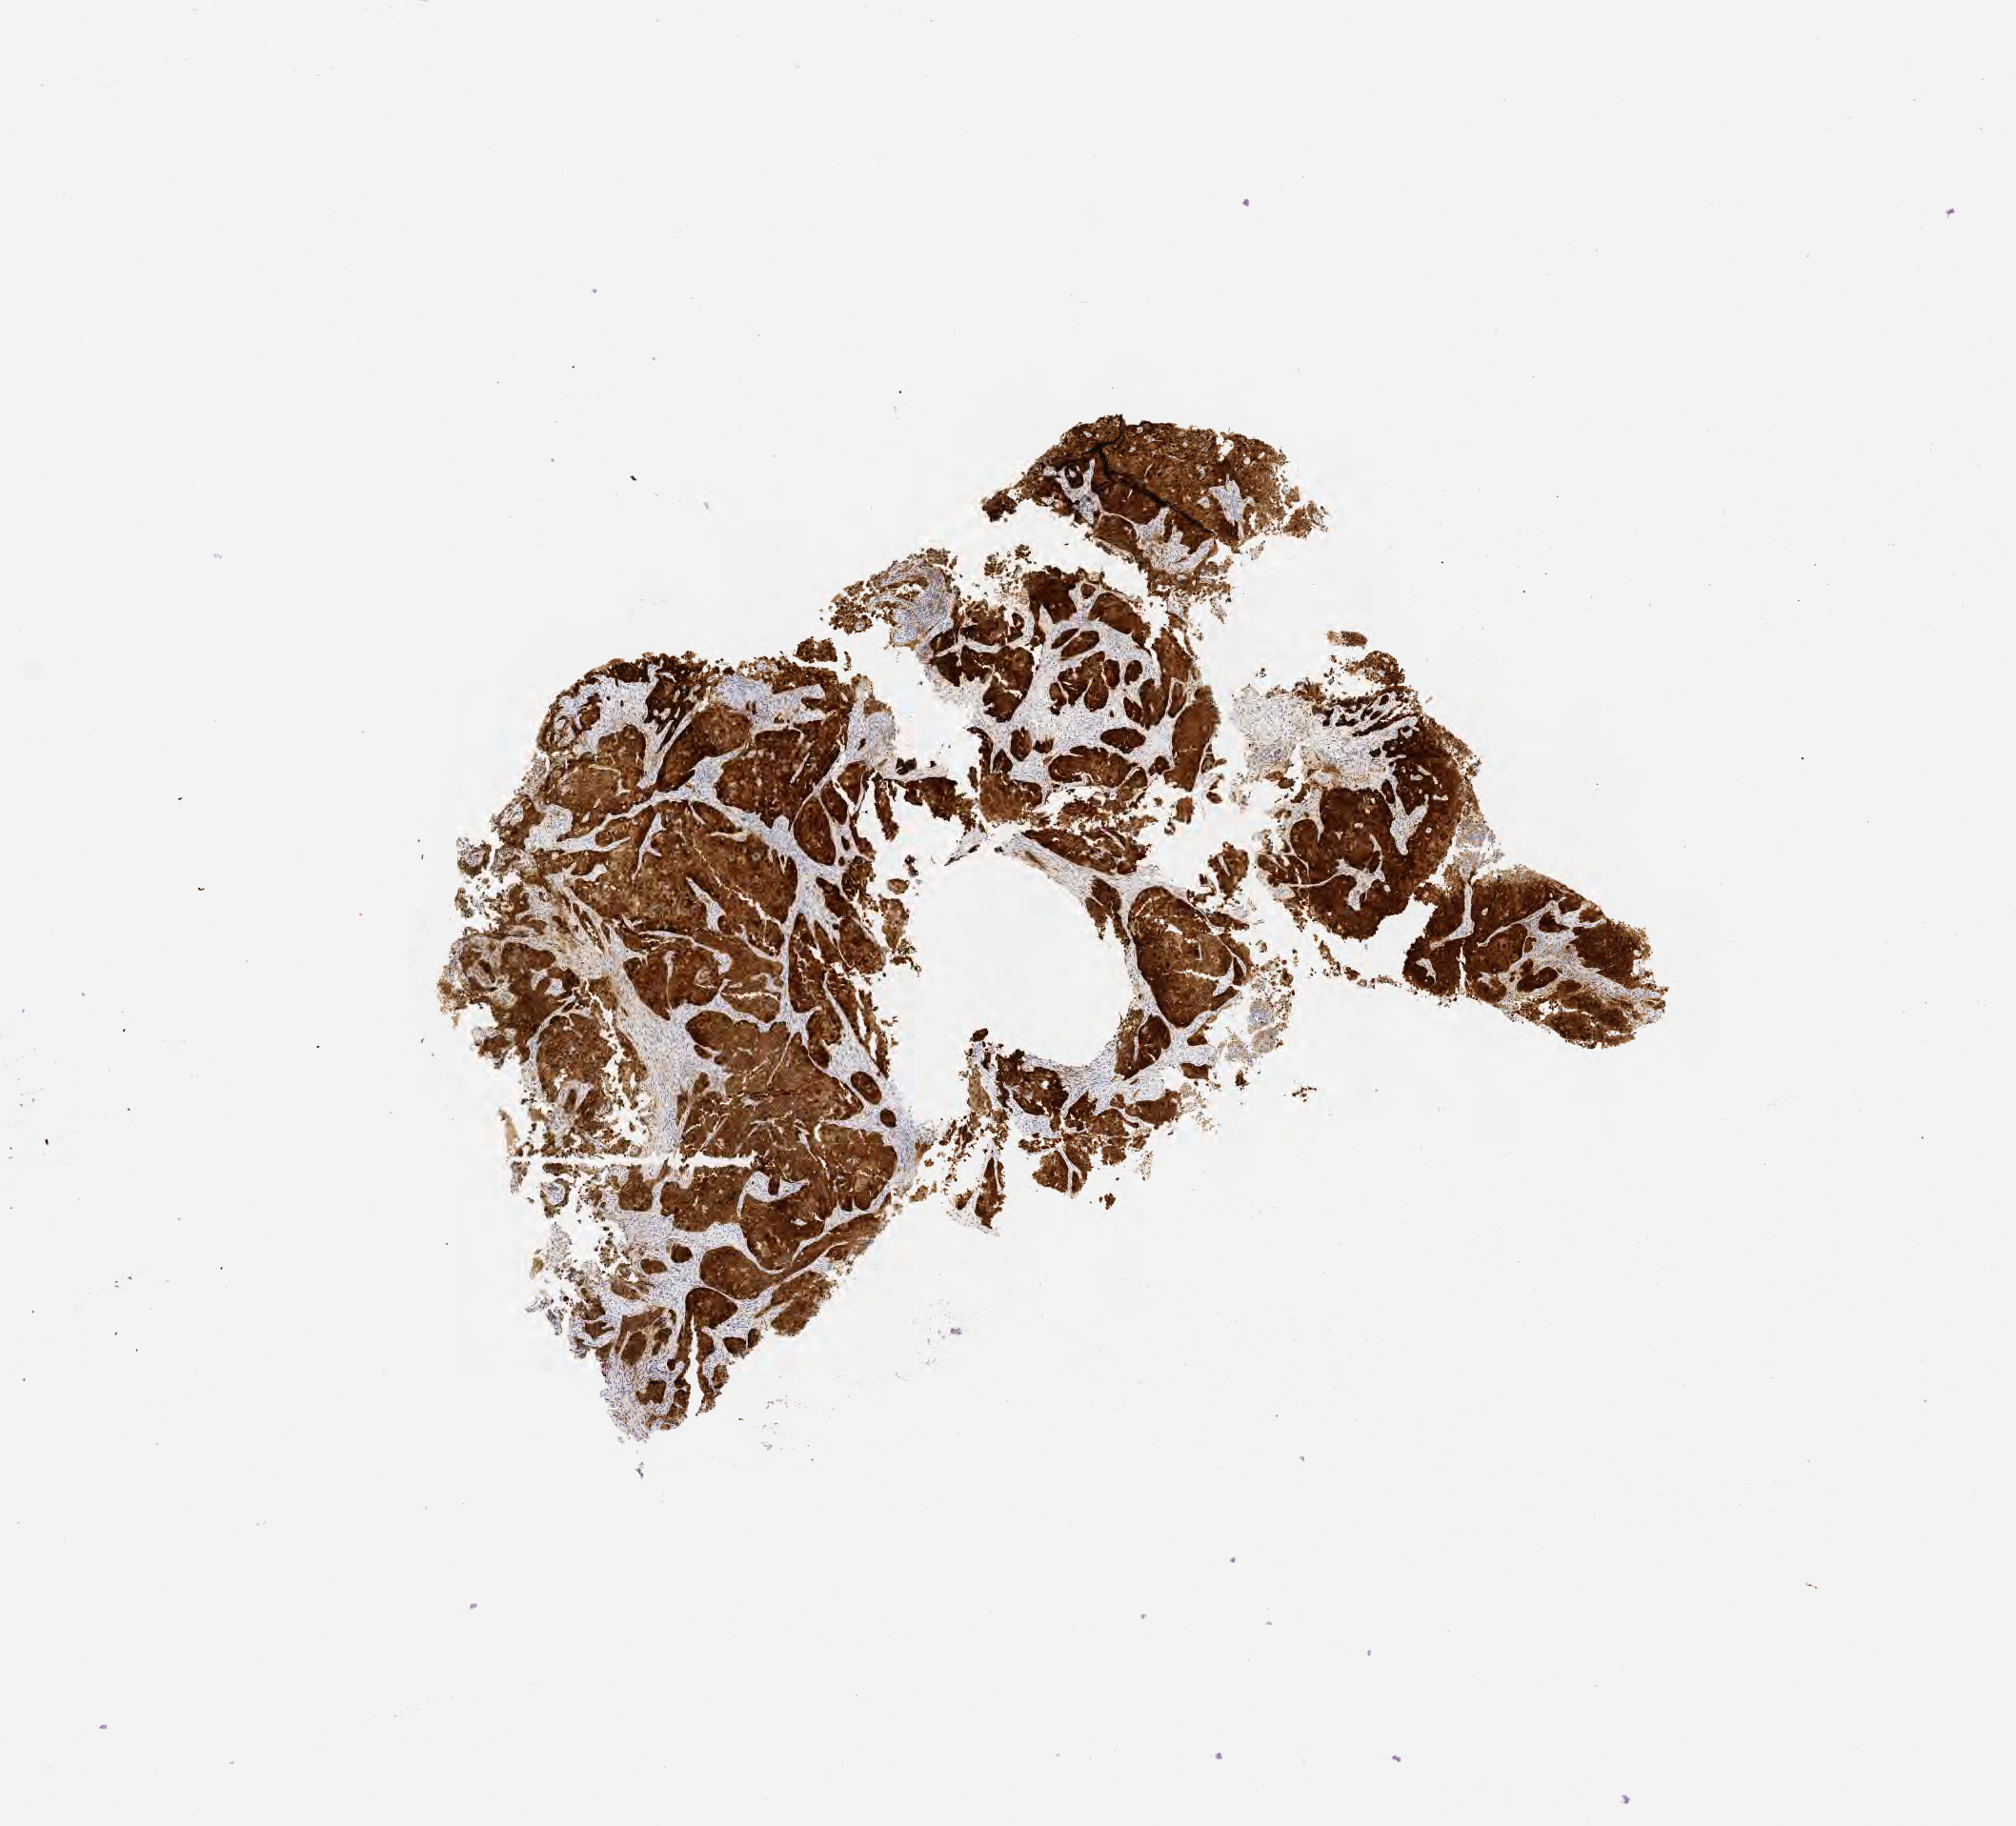
Whole-slide image, immunohistochemical stain for p16 (p16INK4a), whole scanned area (about 8.6 x 7.7 mm) shown as a low-resolution overview; specimen: tumor tissue; anatomic site: cervix. Female patient, age 43 years.
- histologic diagnosis: Squamous cell carcinoma, large cell, nonkeratinizing, NOS